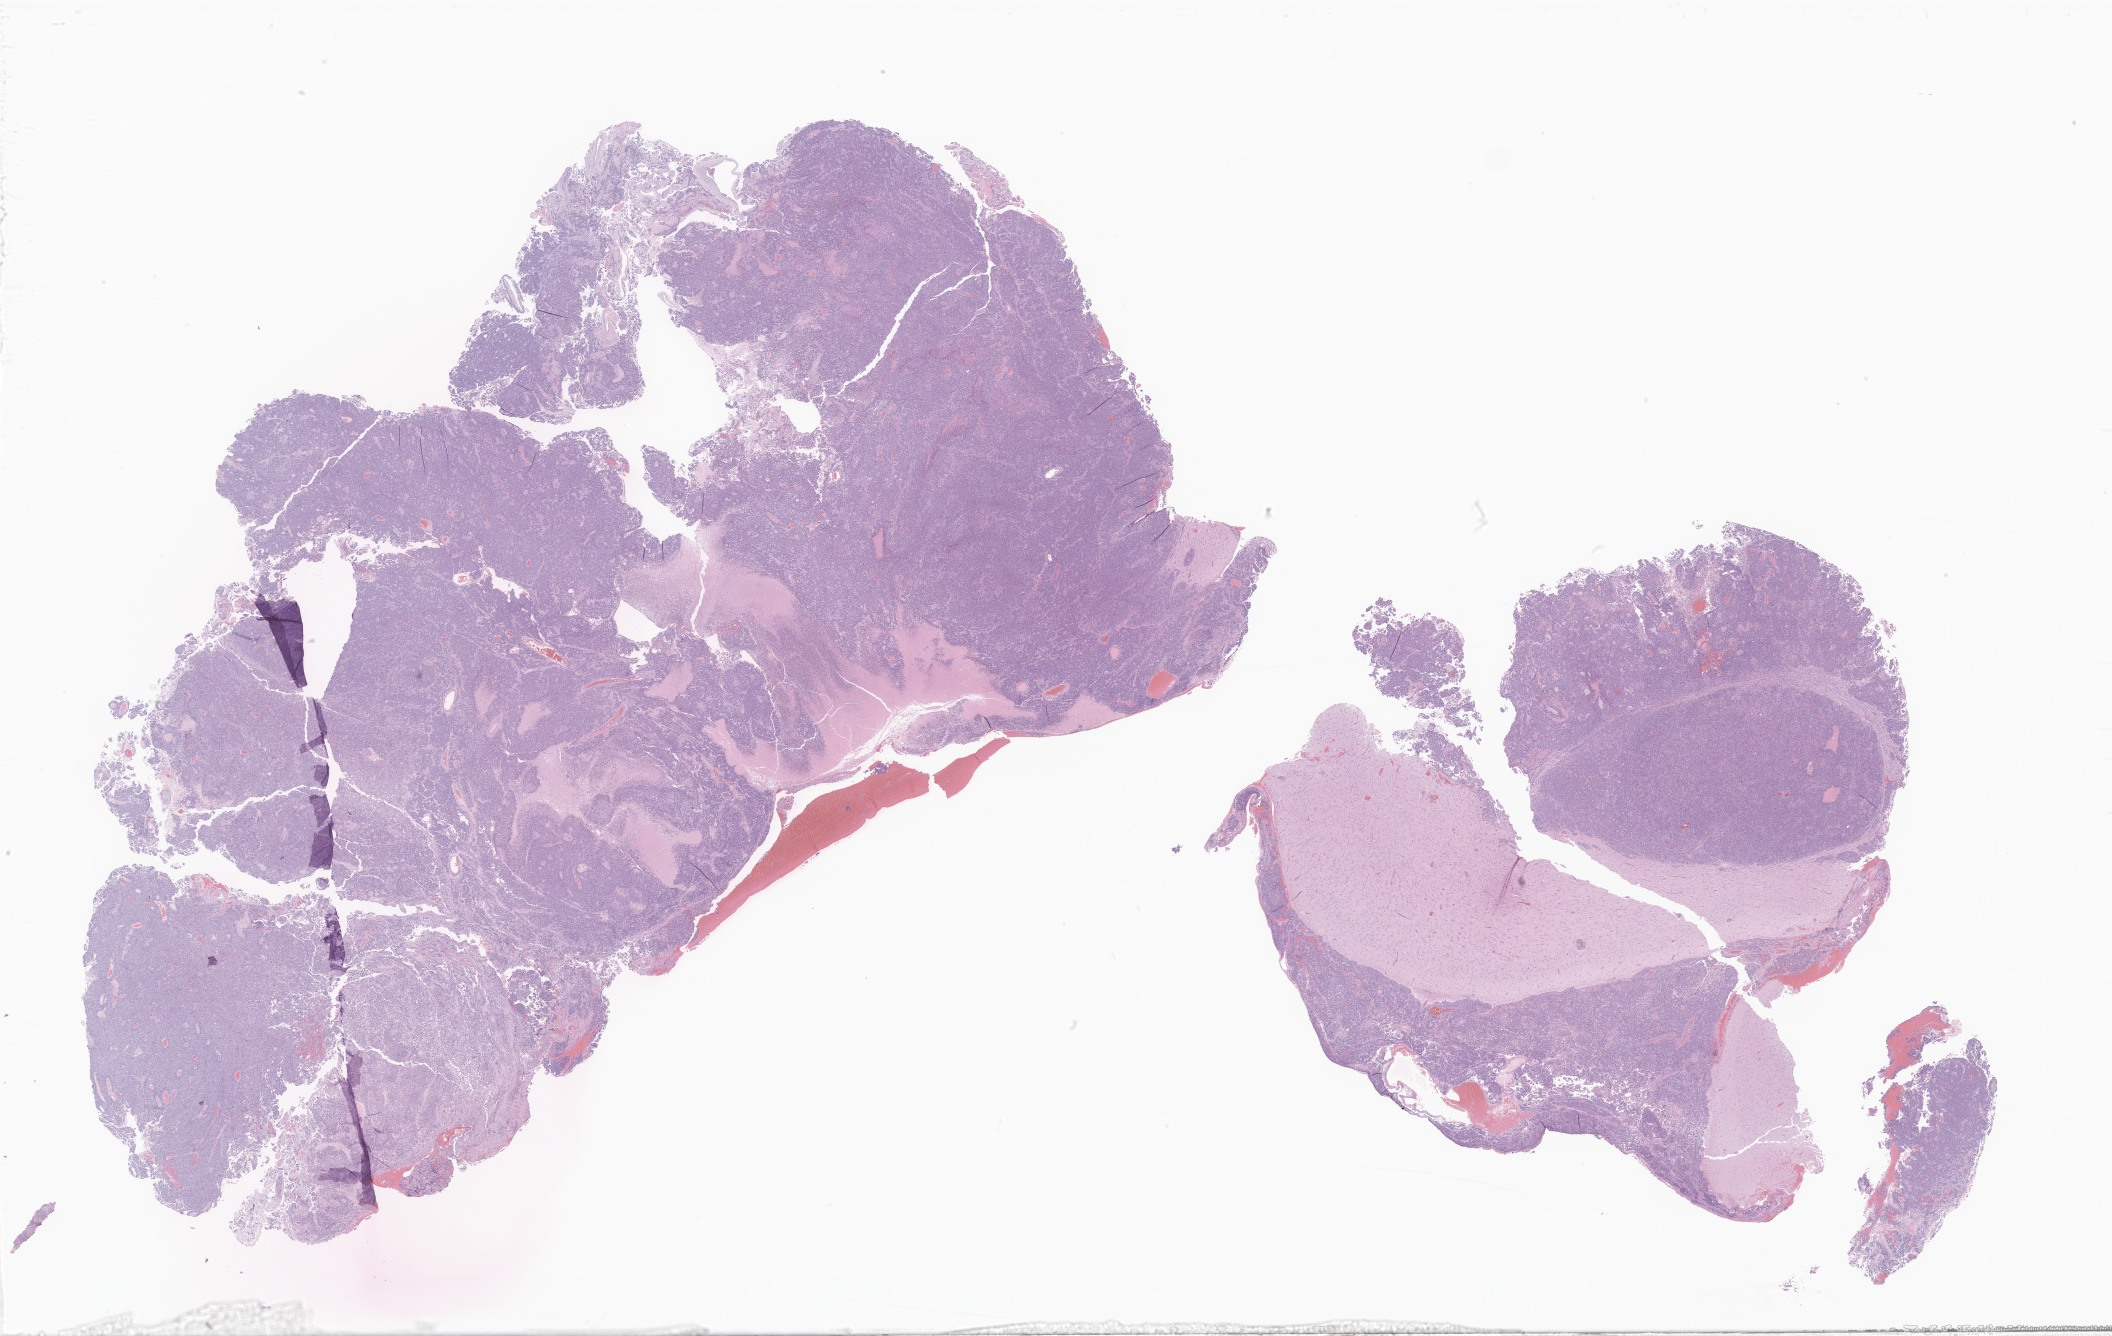
Whole-slide image, haematoxylin and eosin stain of tumor tissue from the lower limb — shown as a low-resolution overview of the whole scanned area (about 35.6 x 22.5 mm); FFPE section. Patient: male, age 325 months (27 years 1 month).
- recorded diagnosis: Embryonal rhabdomyosarcoma, NOS